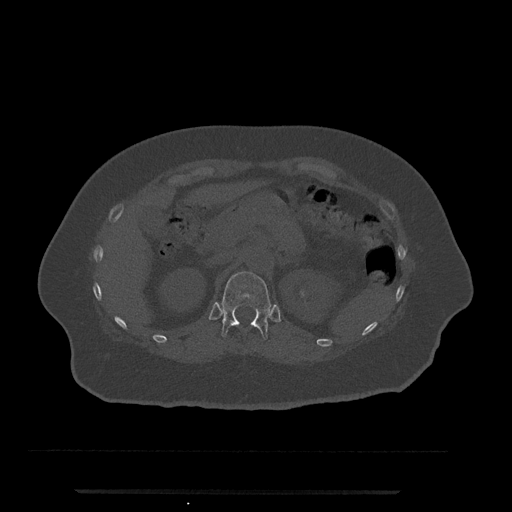
CT including the spine, one axial slice. Position 177 of 797 along the scan axis. Reconstruction kernel Br40s/3. 120 kVp. Bone window (W 1800 / L 400 HU). 0.5 mm slice thickness. 512 × 512 image matrix, field of view 440 × 440 mm. Female patient, age 51 years. Case-level facts recorded for this patient, not image findings: primary cancer: neuro; vertebrae with lytic lesions (as recorded): T8.
Structures marked on this image (semi-automatically segmented with operator editing):
- T12 vertebra: bounding box <221,271,271,340> (left, top, right, bottom; pixels)